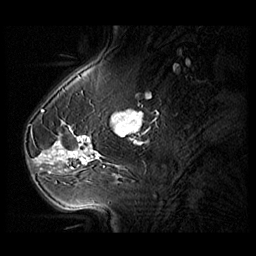
Breast MRI (dynamic contrast-enhanced), one sagittal slice; slice 33 of 104 in the series (ordered by position); 3 images stored at this slice position (order not interpretable as contrast timing); 1.5 T; TE 1.3 ms, TR 5.5 ms; 3 mm slice thickness; 256 × 256 image matrix, field of view 220 × 220 mm. Patient: female, 54 years. Case-level facts recorded for this patient, not image findings: setting: breast cancer imaged before/during neoadjuvant chemotherapy; receptor status: HR-positive, HER2-negative.
Outlined on this slice (semi-automatically segmented with operator editing):
- analysis volume of interest (the breast-tissue region the enhancement analysis was run in; not a lesion): bounding box [x1, y1, x2, y2] px = [28, 127, 104, 182]
- tumour enhancement mask (voxels above the 140 % enhancement threshold inside the analysis volume of interest): [35, 135, 98, 164]